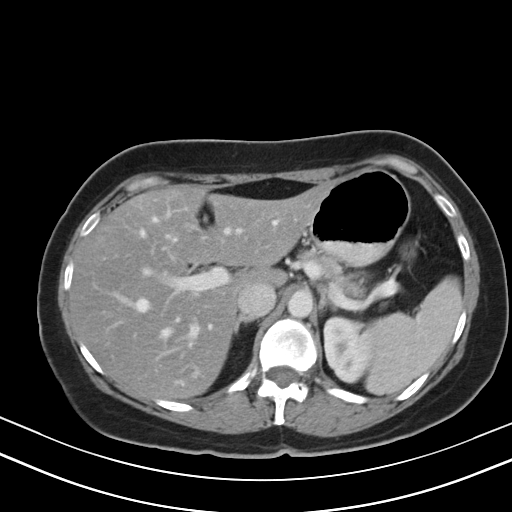
Contrast-enhanced abdominal CT, one axial slice. Position 31 of 47 along the scan axis. 130 kVp. Soft-tissue window (W 400 / L 40 HU). 5 mm slice thickness. 512 × 512 image matrix. Female patient. Case-level facts recorded for this patient, not image findings: diagnosis: colorectal cancer liver metastases, imaged before liver resection; multiple liver metastases: no; largest metastasis: 3.5 cm; disease in both lobes: no.
Structures marked on this image (expert manual segmentation):
- hepatic veins: bounding box [x1, y1, x2, y2] px = [114, 217, 277, 360]
- liver: [71, 187, 325, 398]
- planned liver remnant (the part of the liver to remain after resection): [71, 188, 325, 398]
- portal vein (with intrahepatic branches): [145, 228, 230, 338]